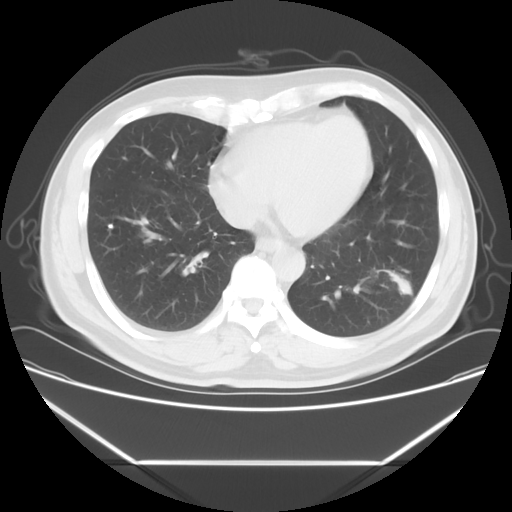
Chest CT, one axial slice; slice 21 of 57 in the series (ordered by position); reconstruction kernel STANDARD; 120 kVp; lung window (W 1500 / L -600 HU); 5 mm slice thickness; 512 × 512 image matrix, field of view 384 × 384 mm. Patient: male, 53 years. From the clinical record (not read from this slice): clinical TNM (as recorded): T1c N0 M0; histopathological grade: G2-3.
Structures marked on this image (bounding box drawn by a radiologist):
- lung tumour (recorded histology: adenocarcinoma): box from (x=378, y=259) to (x=415, y=302) px